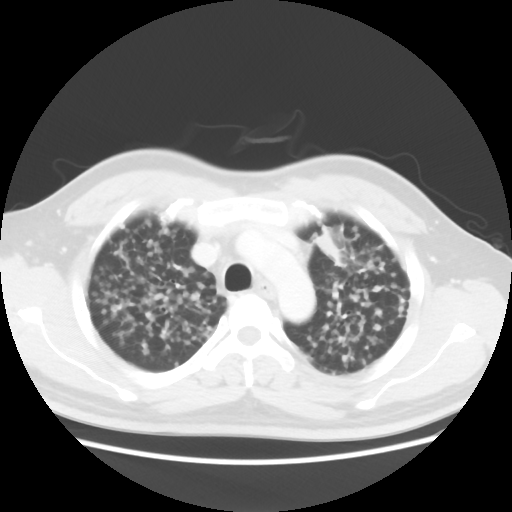
Chest CT, one axial slice; position 30 of 40 along the scan axis; lung window (W 1500 / L -600 HU); 512 × 512 image matrix, field of view 366 × 366 mm. Patient: male, 41 years. From the clinical record (not read from this slice): clinical TNM (as recorded): T1c N3 M1b; histopathological grade: G2-3.
Outlined on this slice (bounding box drawn by a radiologist):
- lung tumour (recorded histology: adenocarcinoma): bounding box <311,224,343,269> (left, top, right, bottom; pixels)